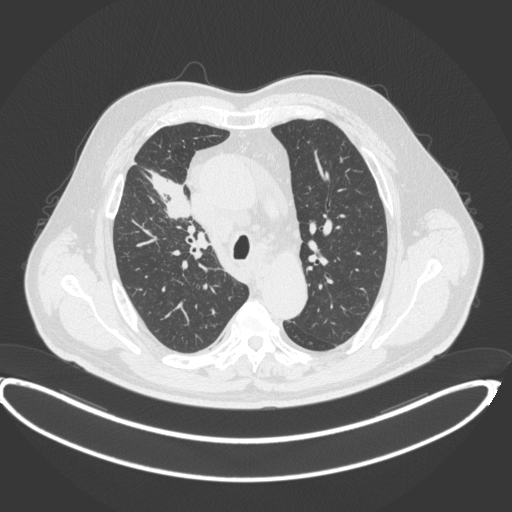
Chest CT, one axial slice; 120 kVp; lung window (W 1500 / L -600 HU); 1 mm slice thickness; 512 × 512 image matrix. Patient: male, 62 years. Case-level facts recorded for this patient, not image findings: clinical TNM (as recorded): T1c N3 M1c.
Structures marked on this image (bounding box drawn by a radiologist):
- lung tumour (recorded histology: adenocarcinoma): bounding box (x1, y1, x2, y2) in pixels: (147, 168, 192, 223)